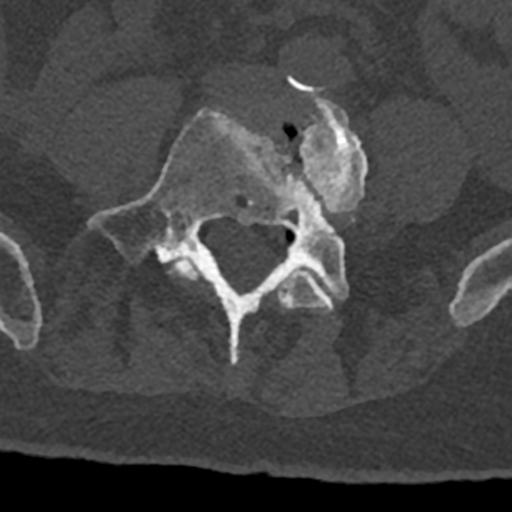
CT including the spine, one axial slice; position 218 of 797 along the scan axis; reconstruction kernel Br40s/3; 120 kVp; bone window (W 1800 / L 400 HU); 0.5 mm slice thickness; 512 × 512 image matrix, field of view 160 × 160 mm. Patient: male, 74 years. From the clinical record (not read from this slice): primary cancer: renal.
Outlined on this slice (semi-automatically segmented with operator editing):
- L4 vertebra: bounding box [x1, y1, x2, y2] px = [170, 93, 368, 315]
- L5 vertebra: [88, 109, 349, 364]